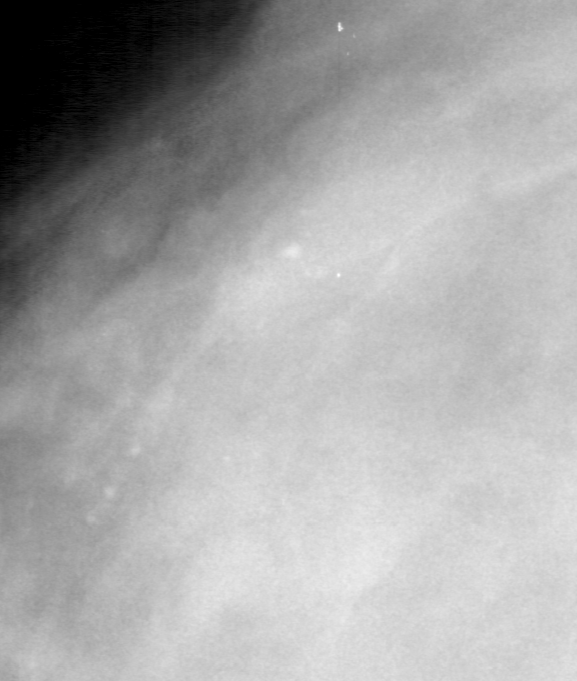
Crop from a digitized film mammogram around one marked abnormality, left breast, CC view.
Marked abnormality: calcifications, morphology pleomorphic, distribution linear; BI-RADS assessment category 4; subtlety rating 4 on a 1 (subtle) to 5 (obvious) scale; pathology result (as recorded, not read from the image): benign.